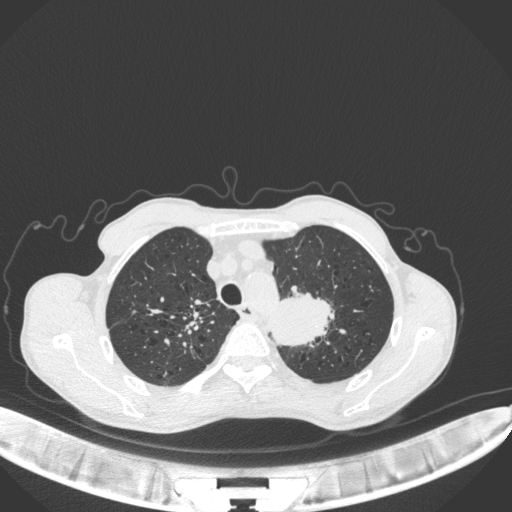
Chest CT, one axial slice; position 341 of 394 along the scan axis; reconstruction kernel B31f; lung window (W 1500 / L -600 HU); 1 mm slice thickness; 512 × 512 image matrix, field of view 400 × 400 mm. Patient: male, 65 years. Case-level facts recorded for this patient, not image findings: clinical TNM (as recorded): T2b N0 M0; histopathological grade: G2.
Annotated regions visible in this slice (rectangle marked by the reading radiologist):
- lung tumour (recorded histology: adenocarcinoma): box from (x=264, y=282) to (x=340, y=351) px